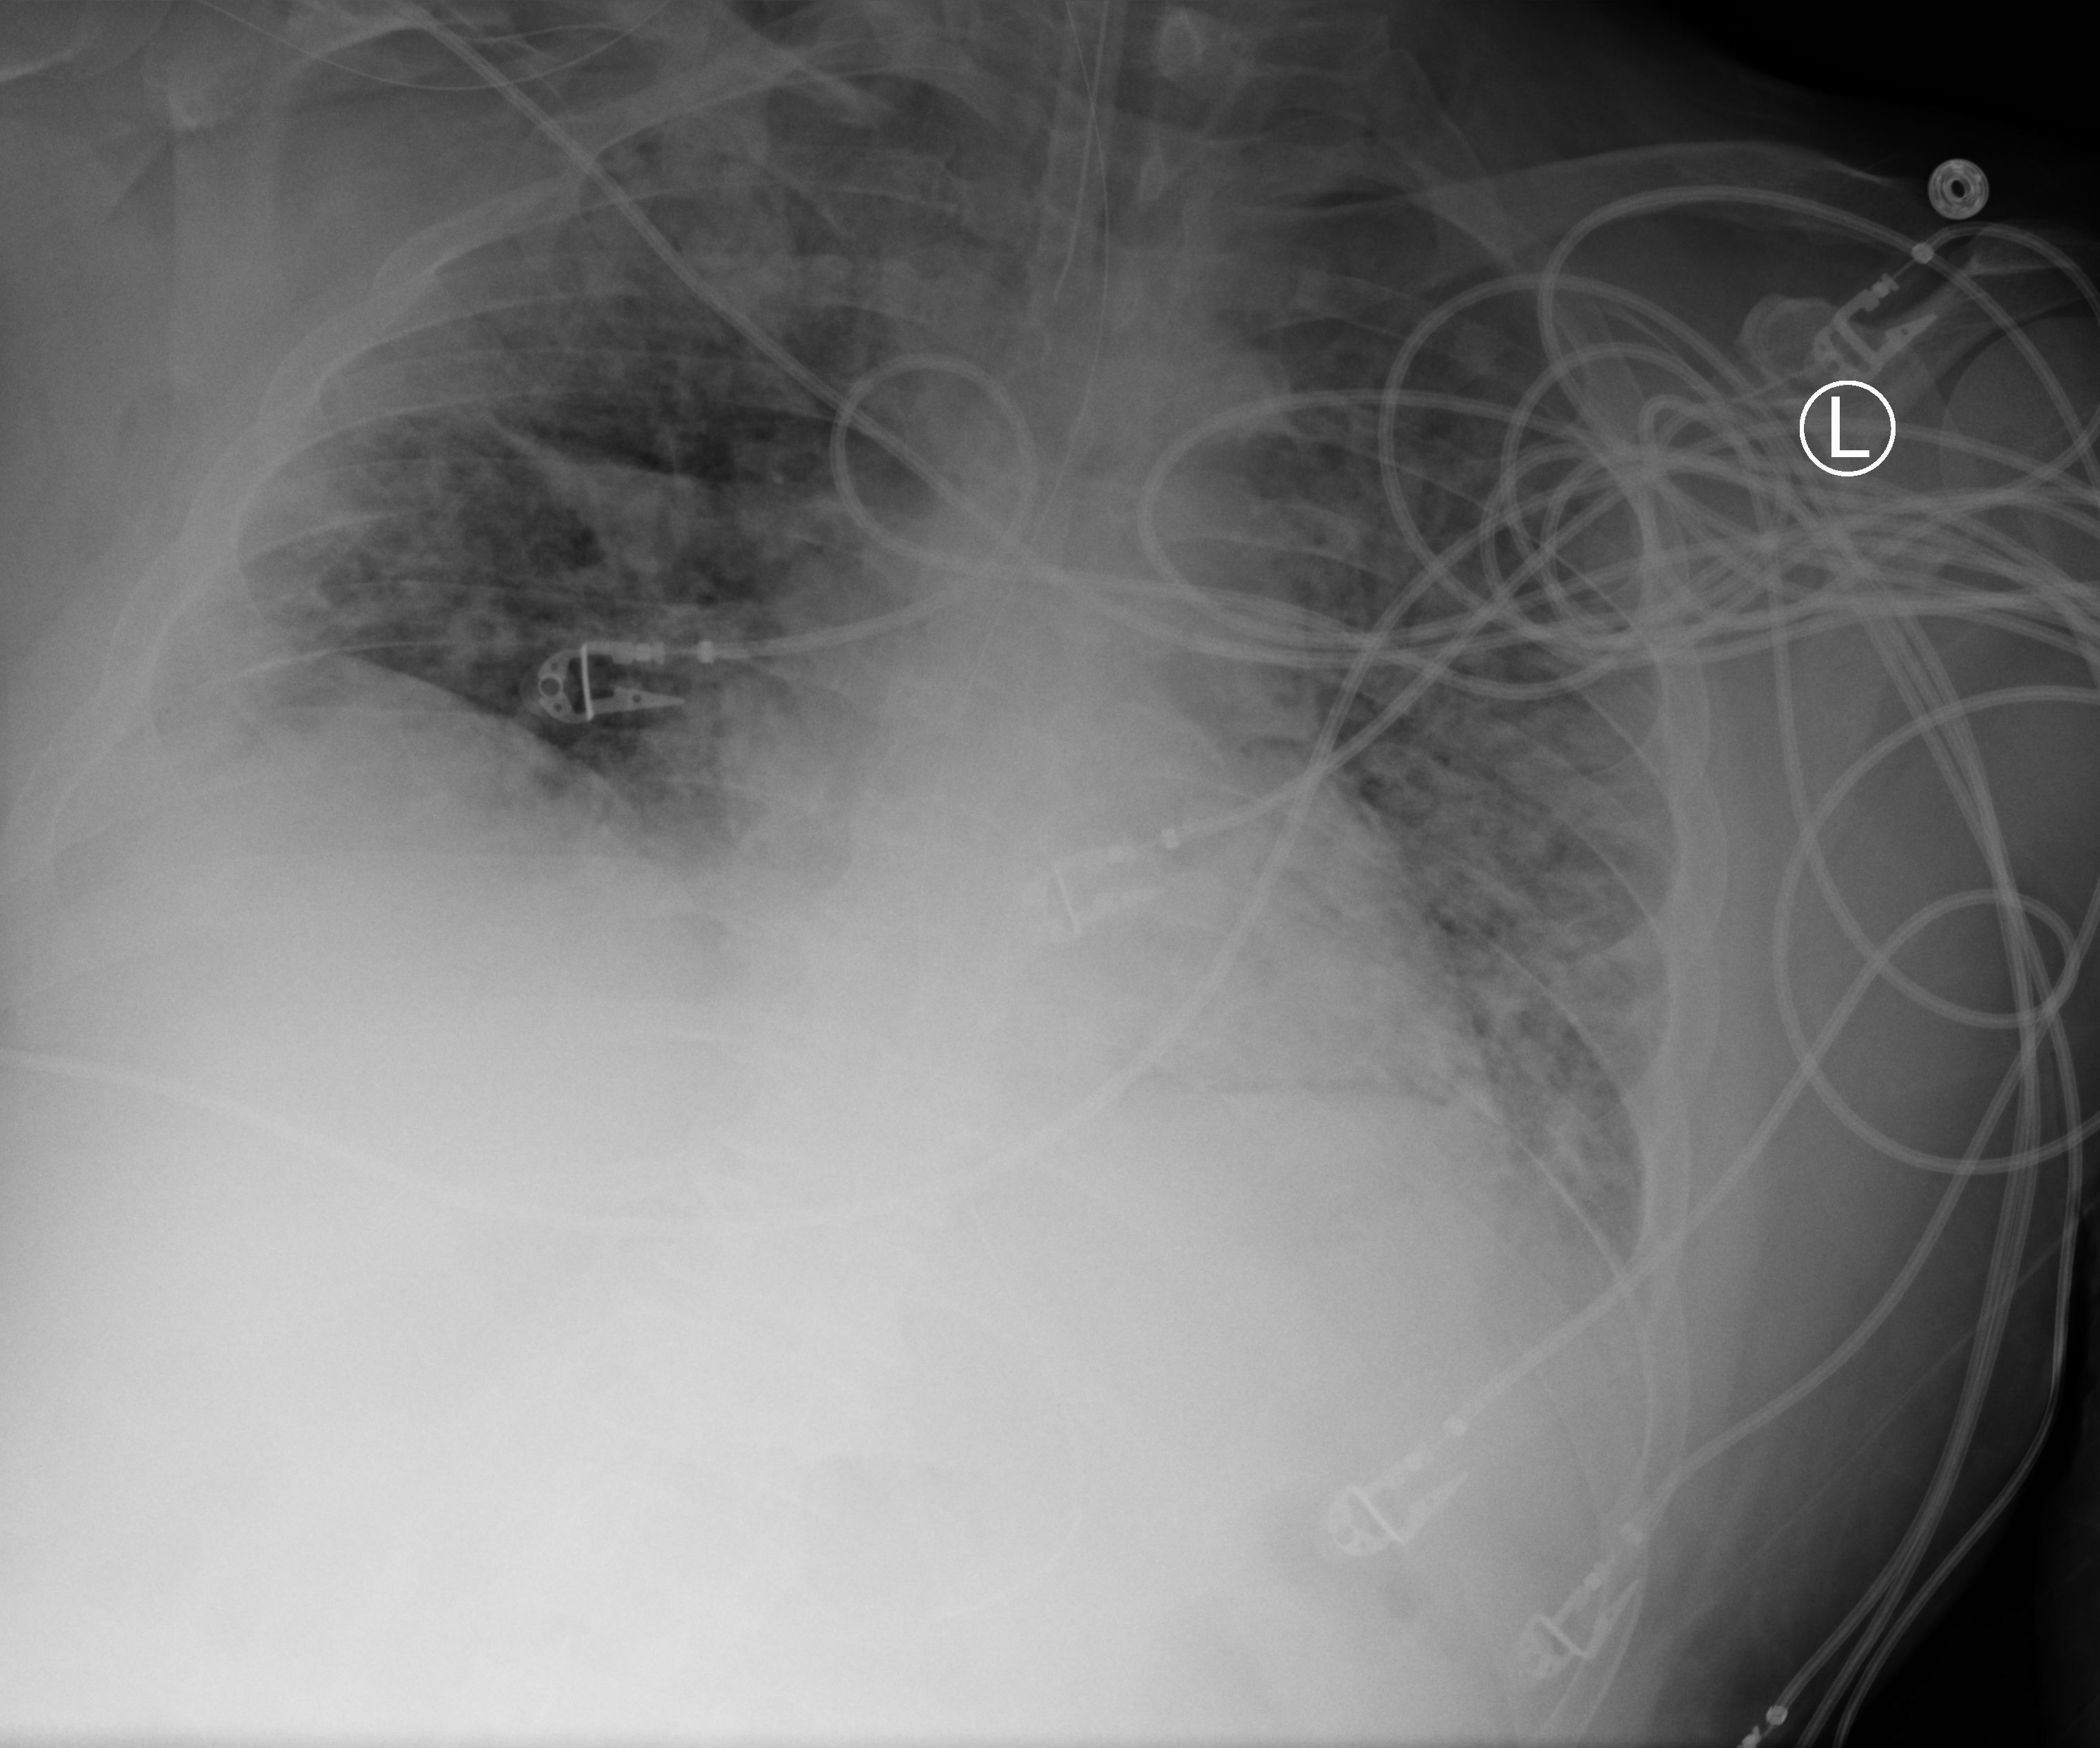
Chest X-ray (portable); anteroposterior (AP) projection. Patient hospitalised with COVID-19, aged 18–59 years.
From the hospital-stay record, not from the radiograph (when in the stay this image was taken is not recorded):
- admitted to intensive care during this hospital stay: yes
- mechanically ventilated during this hospital stay: yes